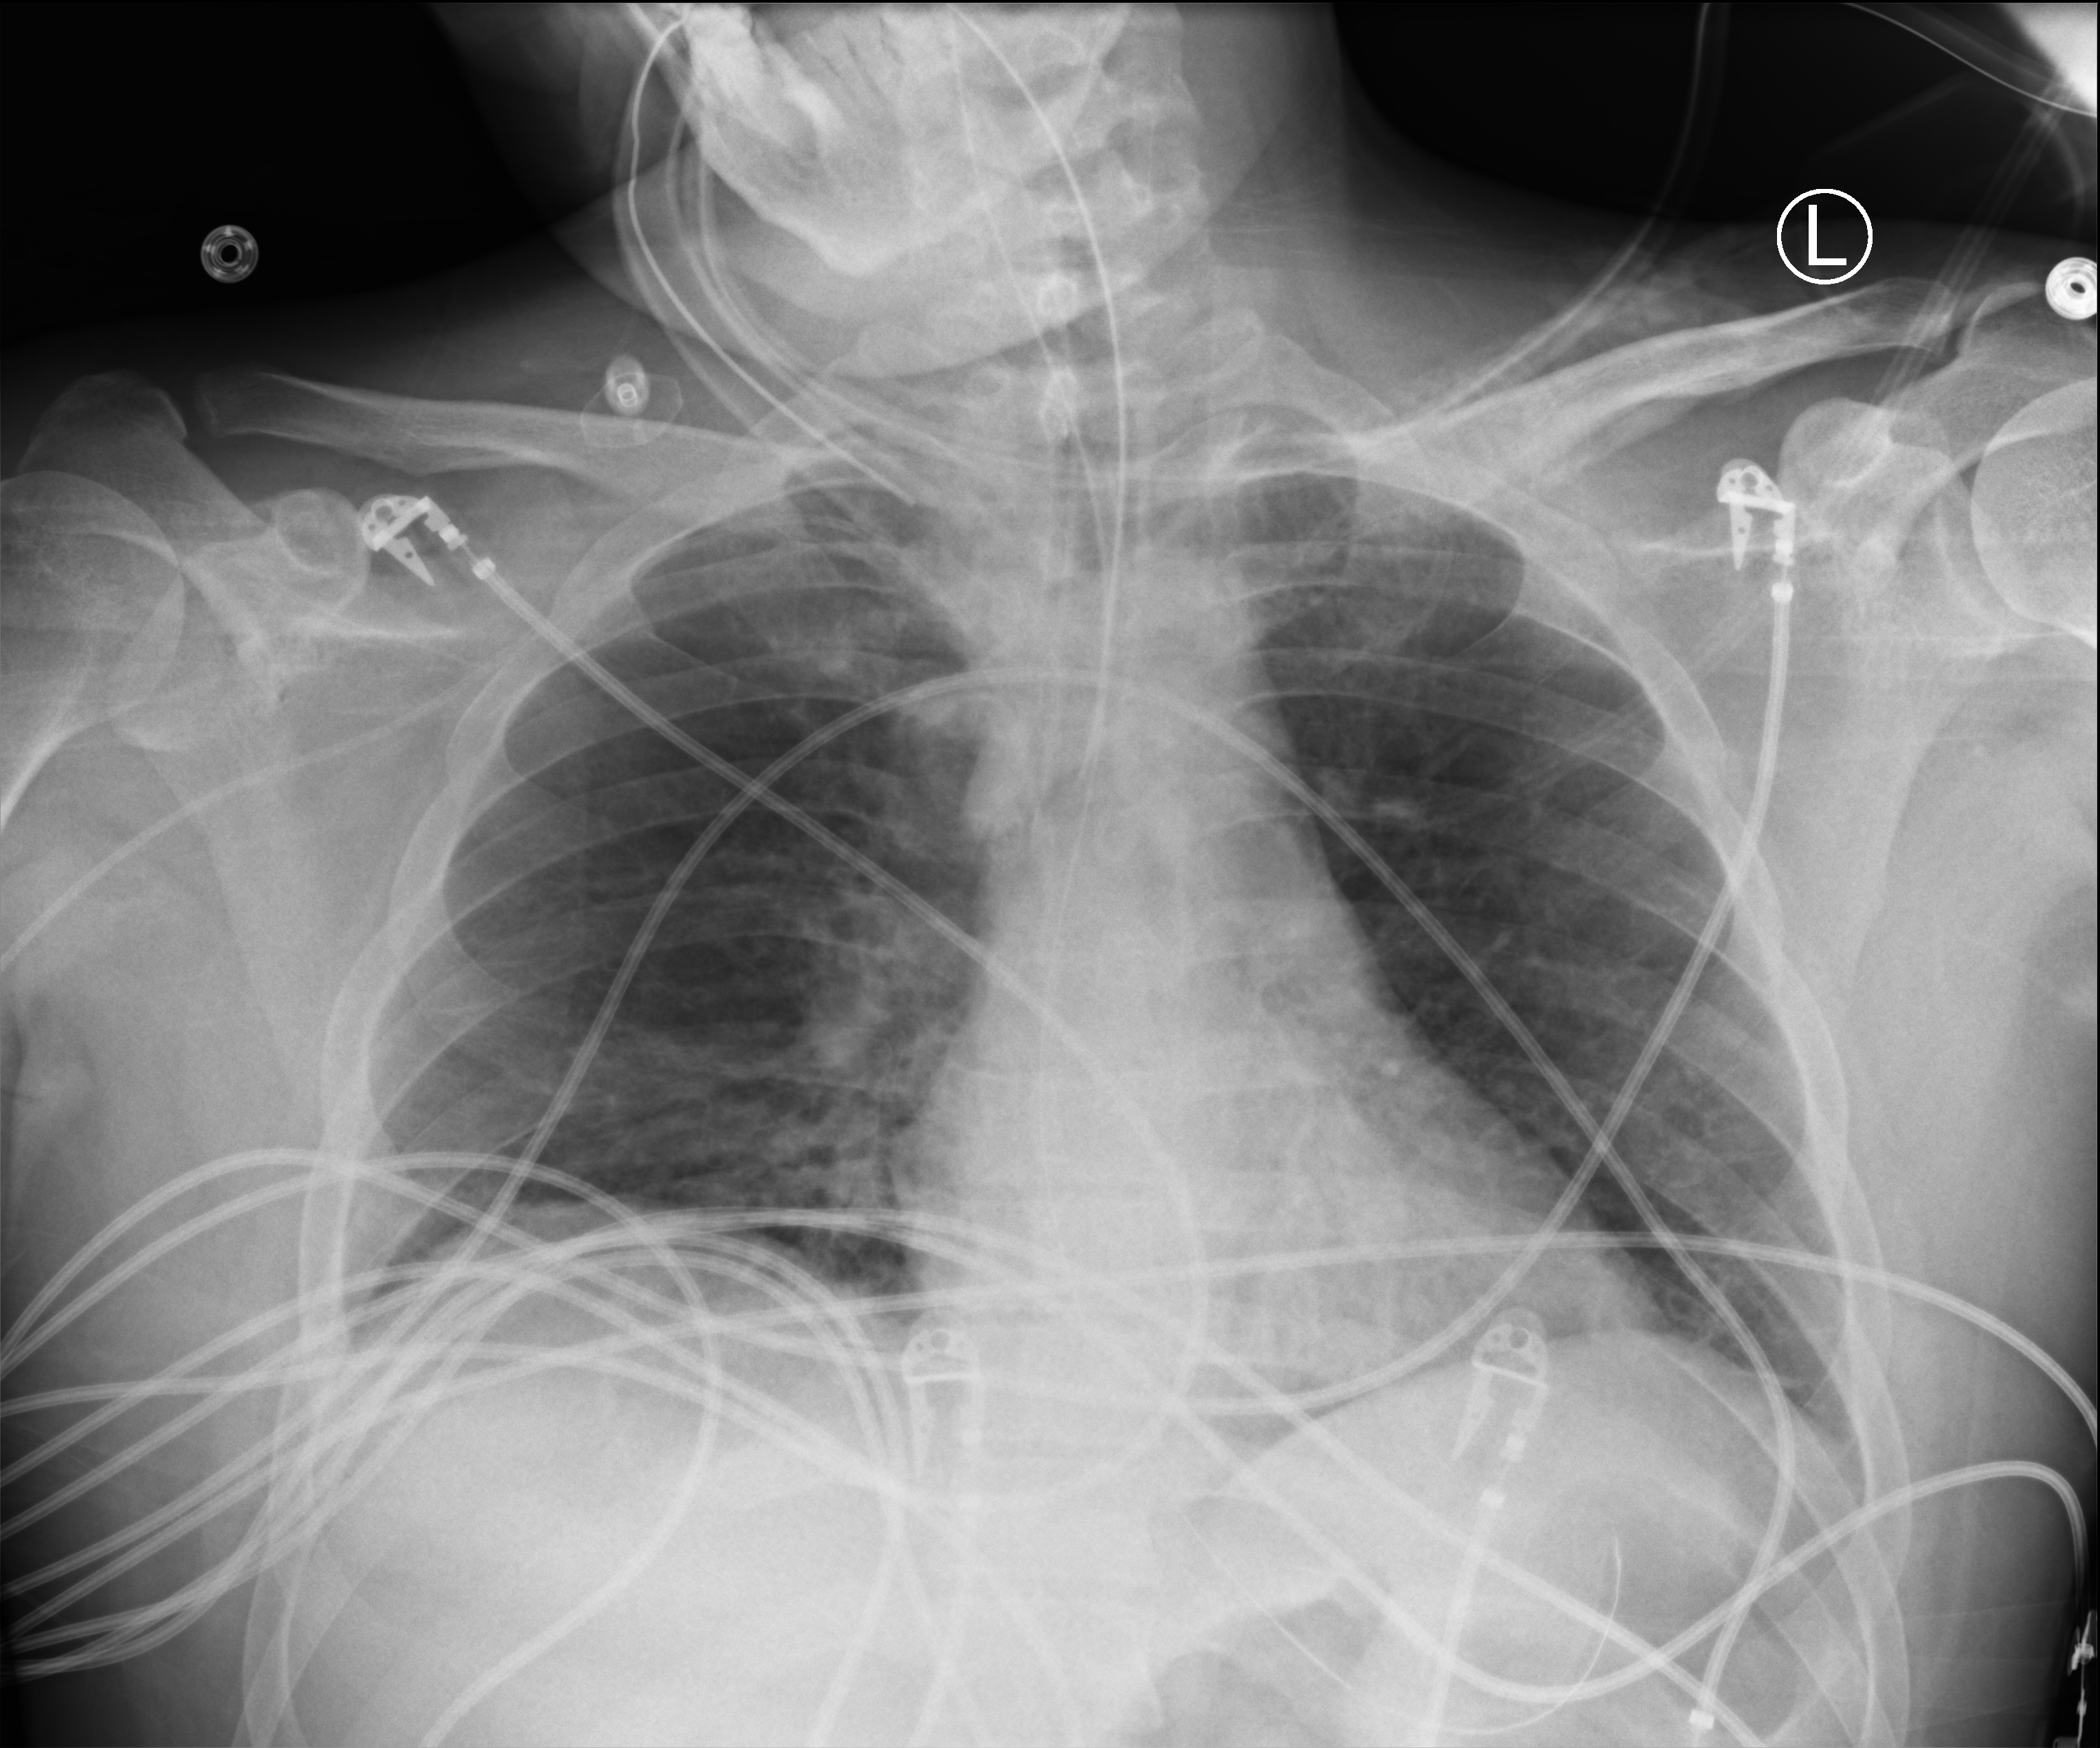
Portable chest radiograph; anteroposterior (AP) projection. Patient hospitalised with COVID-19; male, aged 18–59 years.
Admission-level facts for this patient (not findings on this image; timing relative to this image not recorded):
- mechanically ventilated during this hospital stay: yes
- admitted to intensive care during this hospital stay: yes
- length of hospital stay: 44 days